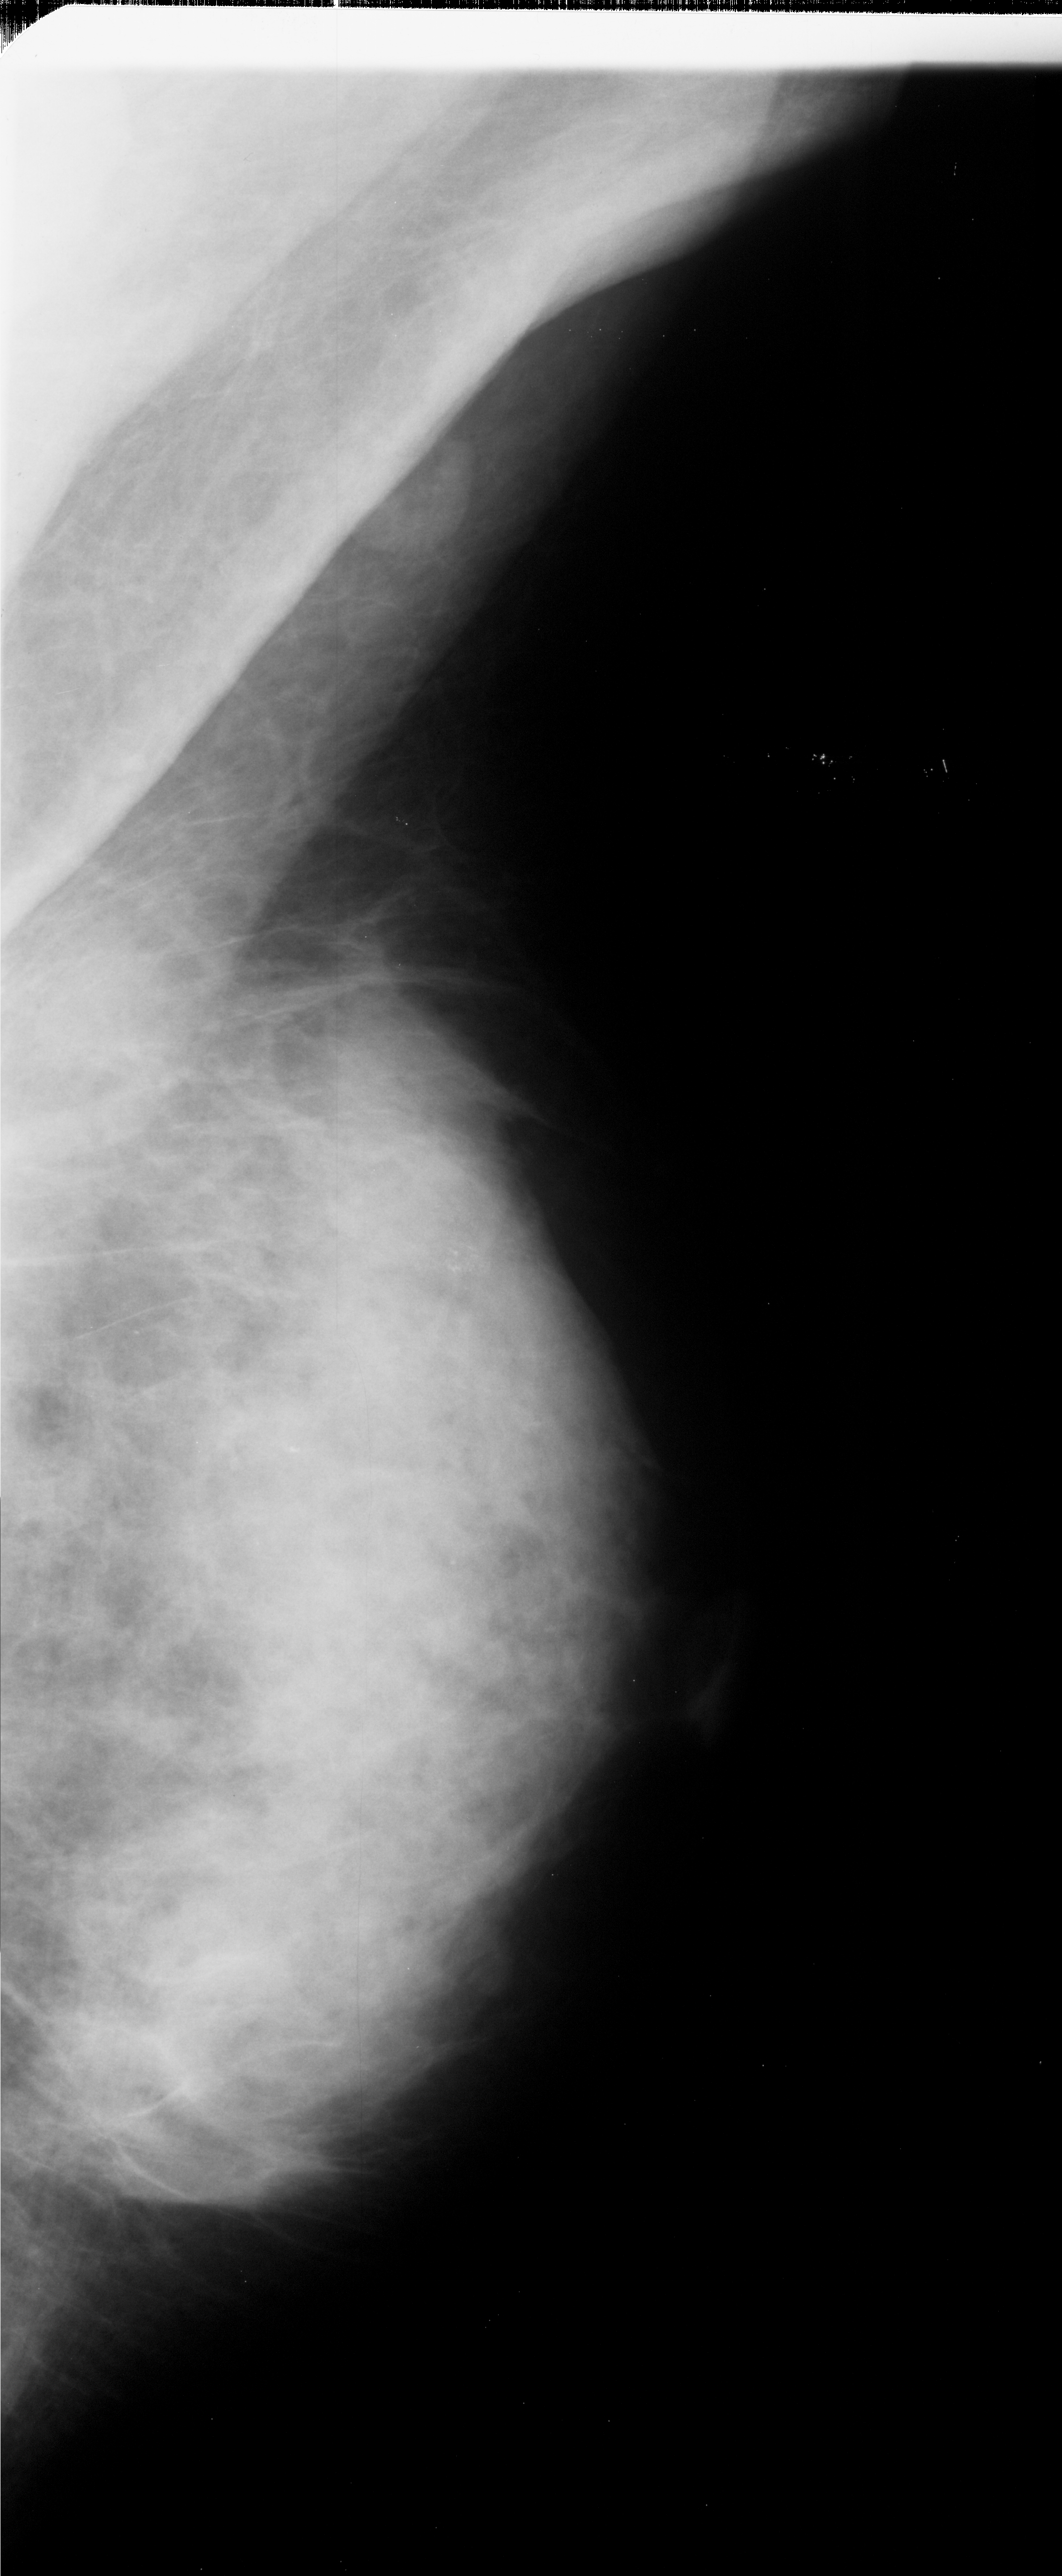
Digitized screen-film mammogram, right breast, MLO view.
Radiologist-marked abnormalities on this image: calcifications, morphology pleomorphic, distribution clustered; BI-RADS assessment category 4; pathology (as recorded): malignant.